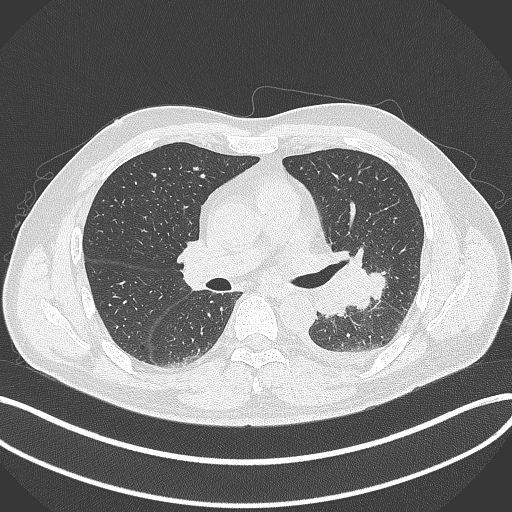
Chest CT, one axial slice. Slice 202 of 342 in the series (ordered by position). Reconstruction kernel B70f. 120 kVp. Lung window (W 1500 / L -600 HU). 512 × 512 image matrix, field of view 400 × 400 mm. Patient: male, 58 years. From the clinical record (not read from this slice): clinical TNM (as recorded): T3 N1 M1b; histopathological grade: G3.
Structures marked on this image (bounding box drawn by a radiologist):
- lung tumour (recorded histology: small cell carcinoma): box from (x=333, y=256) to (x=387, y=315) px